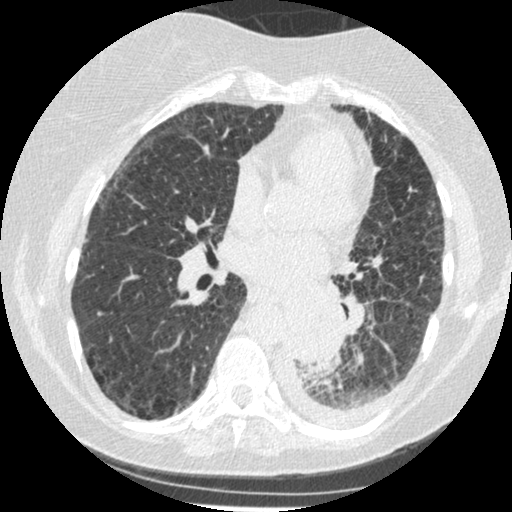
Low-dose screening chest CT, one axial slice. Slice 114 of 341 in the series (ordered by position). Reconstruction kernel STANDARD. 120 kVp. Lung window (W 1500 / L -600 HU). 512 × 512 image matrix, field of view 310 × 310 mm.
Structures marked on this image (outlined manually by an expert reader):
- lesion 1 (tumor, lower lobe of left lung): bounding box [x1, y1, x2, y2] px = [284, 302, 342, 365]